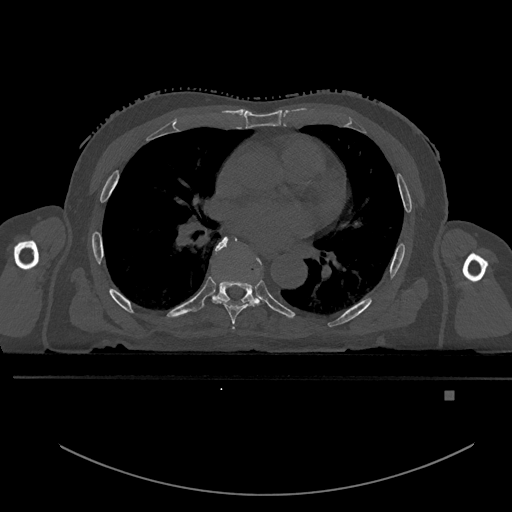
CT including the spine, one axial slice; slice 282 of 969 in the series (ordered by position); bone window (W 1800 / L 400 HU); 0.5 mm slice thickness; 512 × 512 image matrix, field of view 456 × 456 mm. Patient: male, 82 years. Case-level facts recorded for this patient, not image findings: primary cancer: prostate; vertebrae with lytic lesions (as recorded): T11, T9, T8, T2.
Annotated regions visible in this slice (semi-automatic segmentation, software-assisted and operator-edited):
- T5 vertebra: box from (x=232, y=327) to (x=235, y=330) px
- T6 vertebra: (x=211, y=236)–(x=260, y=325)
- T7 vertebra: (x=214, y=261)–(x=261, y=303)